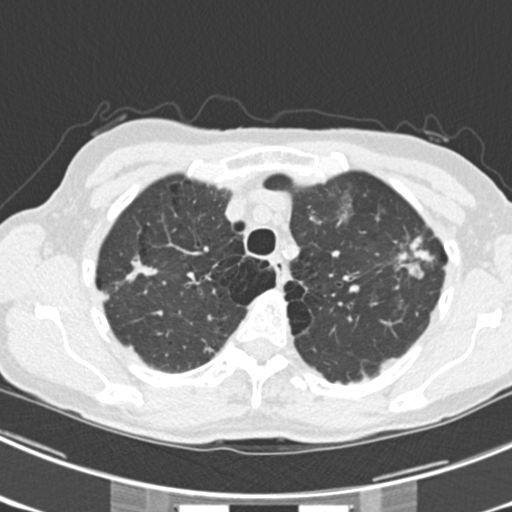
Chest CT (low-dose screening protocol), one axial image. Third screening round (two years after baseline). Lung window (W 1500 / L -600 HU). Standard (soft-tissue) reconstruction kernel (B30f). 512 × 512 image matrix. Female, age 63 years at enrolment. Current smoker at enrolment.
- Expert-annotated lung lesion, box from (x=377, y=223) to (x=449, y=284) px.
- The screening reader recorded 9 non-calcified nodules or masses ≥4 mm on this exam (left upper lobe, right upper lobe, left upper lobe, left lower lobe, right middle lobe, left lower lobe, left lower lobe, right lower lobe, right lower lobe); which of them this box marks is not recorded.
- Official screen result: positive, other.
- Later outcome: lung cancer diagnosed 15 days after this screen — bronchiolo-alveolar adenocarcinoma, NOS, right upper lobe, right middle lobe, right lower lobe, left upper lobe, left lower lobe, moderately differentiated (G2), stage IV (AJCC 6th edition).